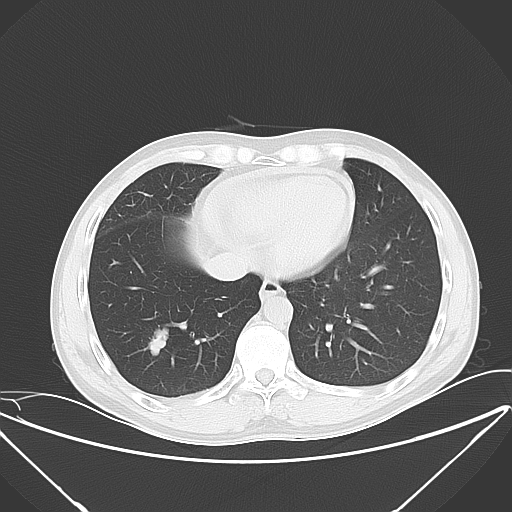
Chest CT, one axial slice; position 17 of 56 along the scan axis; lung window (W 1500 / L -600 HU); 5 mm slice thickness; 512 × 512 image matrix, field of view 397 × 397 mm. Patient: male, 42 years. Case-level facts recorded for this patient, not image findings: clinical TNM (as recorded): T1b N3 M1b.
Outlined on this slice (rectangle marked by the reading radiologist):
- lung tumour (recorded histology: small cell carcinoma): bounding box <140,324,178,369> (left, top, right, bottom; pixels)